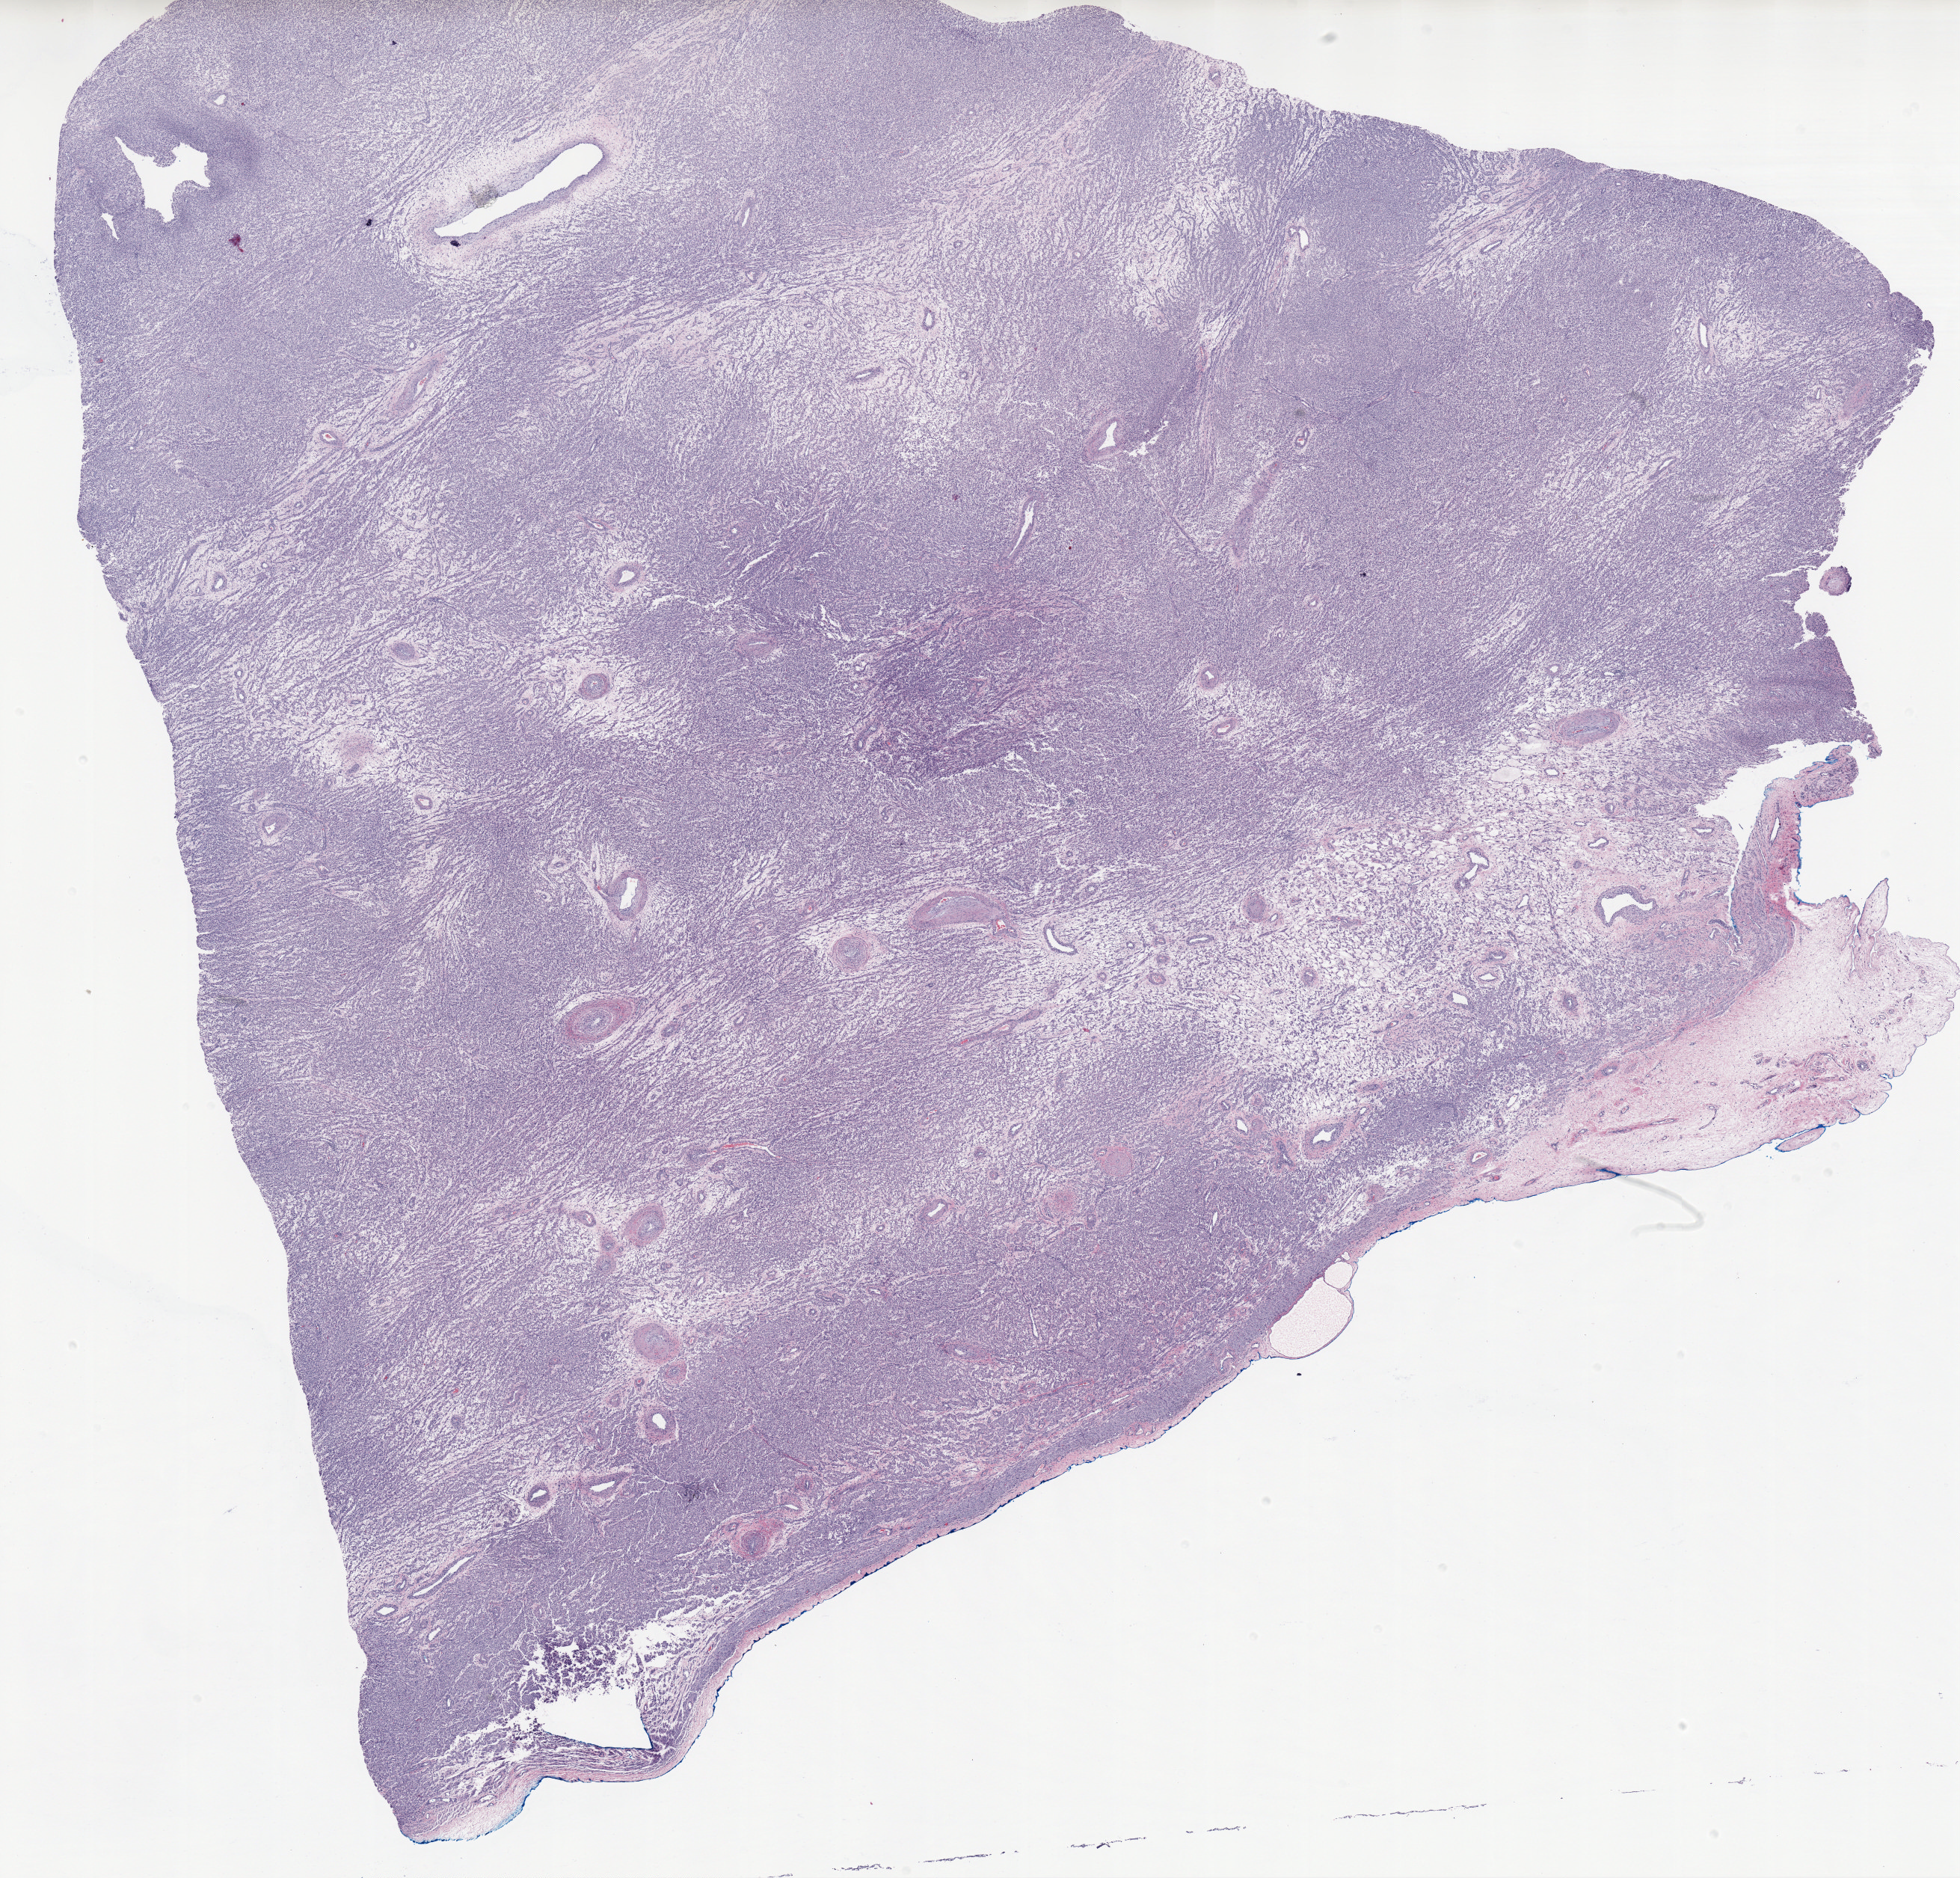
Hematoxylin and eosin (H&E) stained whole-slide image, whole scanned area (about 20.9 x 20.0 mm) shown as a low-resolution overview, formalin-fixed paraffin-embedded (FFPE) diagnostic section, primary tumour sample from the uterus. Patient: female, age at initial diagnosis 44 years.
• histologic diagnosis: Myxoid leiomyosarcoma